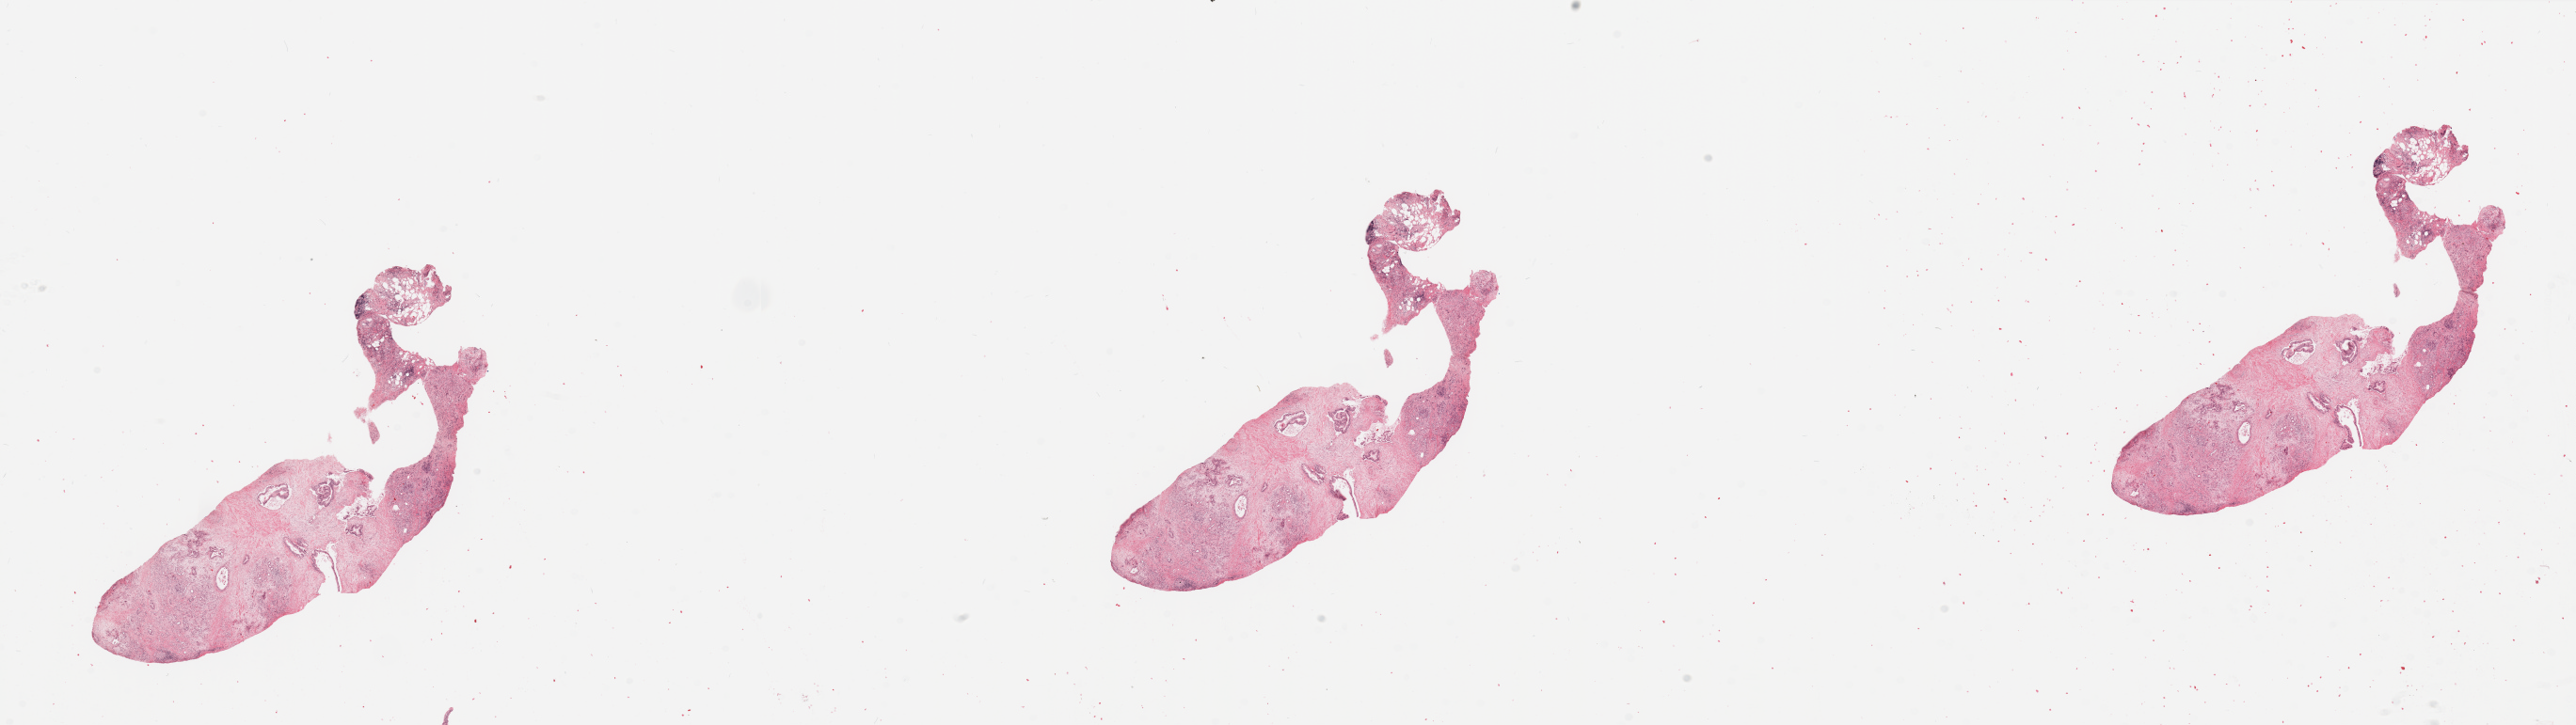
Whole-slide histology image, H&E — a low-resolution overview of the entire scanned area, about 43.3 x 12.2 mm, tumour tissue sample, pancreas. Patient: female, age 77 years. Histologic grade: G2 (moderately differentiated).
• diagnosis: Infiltrating duct carcinoma, NOS
• primary tumour site (as recorded): head
• AJCC pathologic stage: IIB